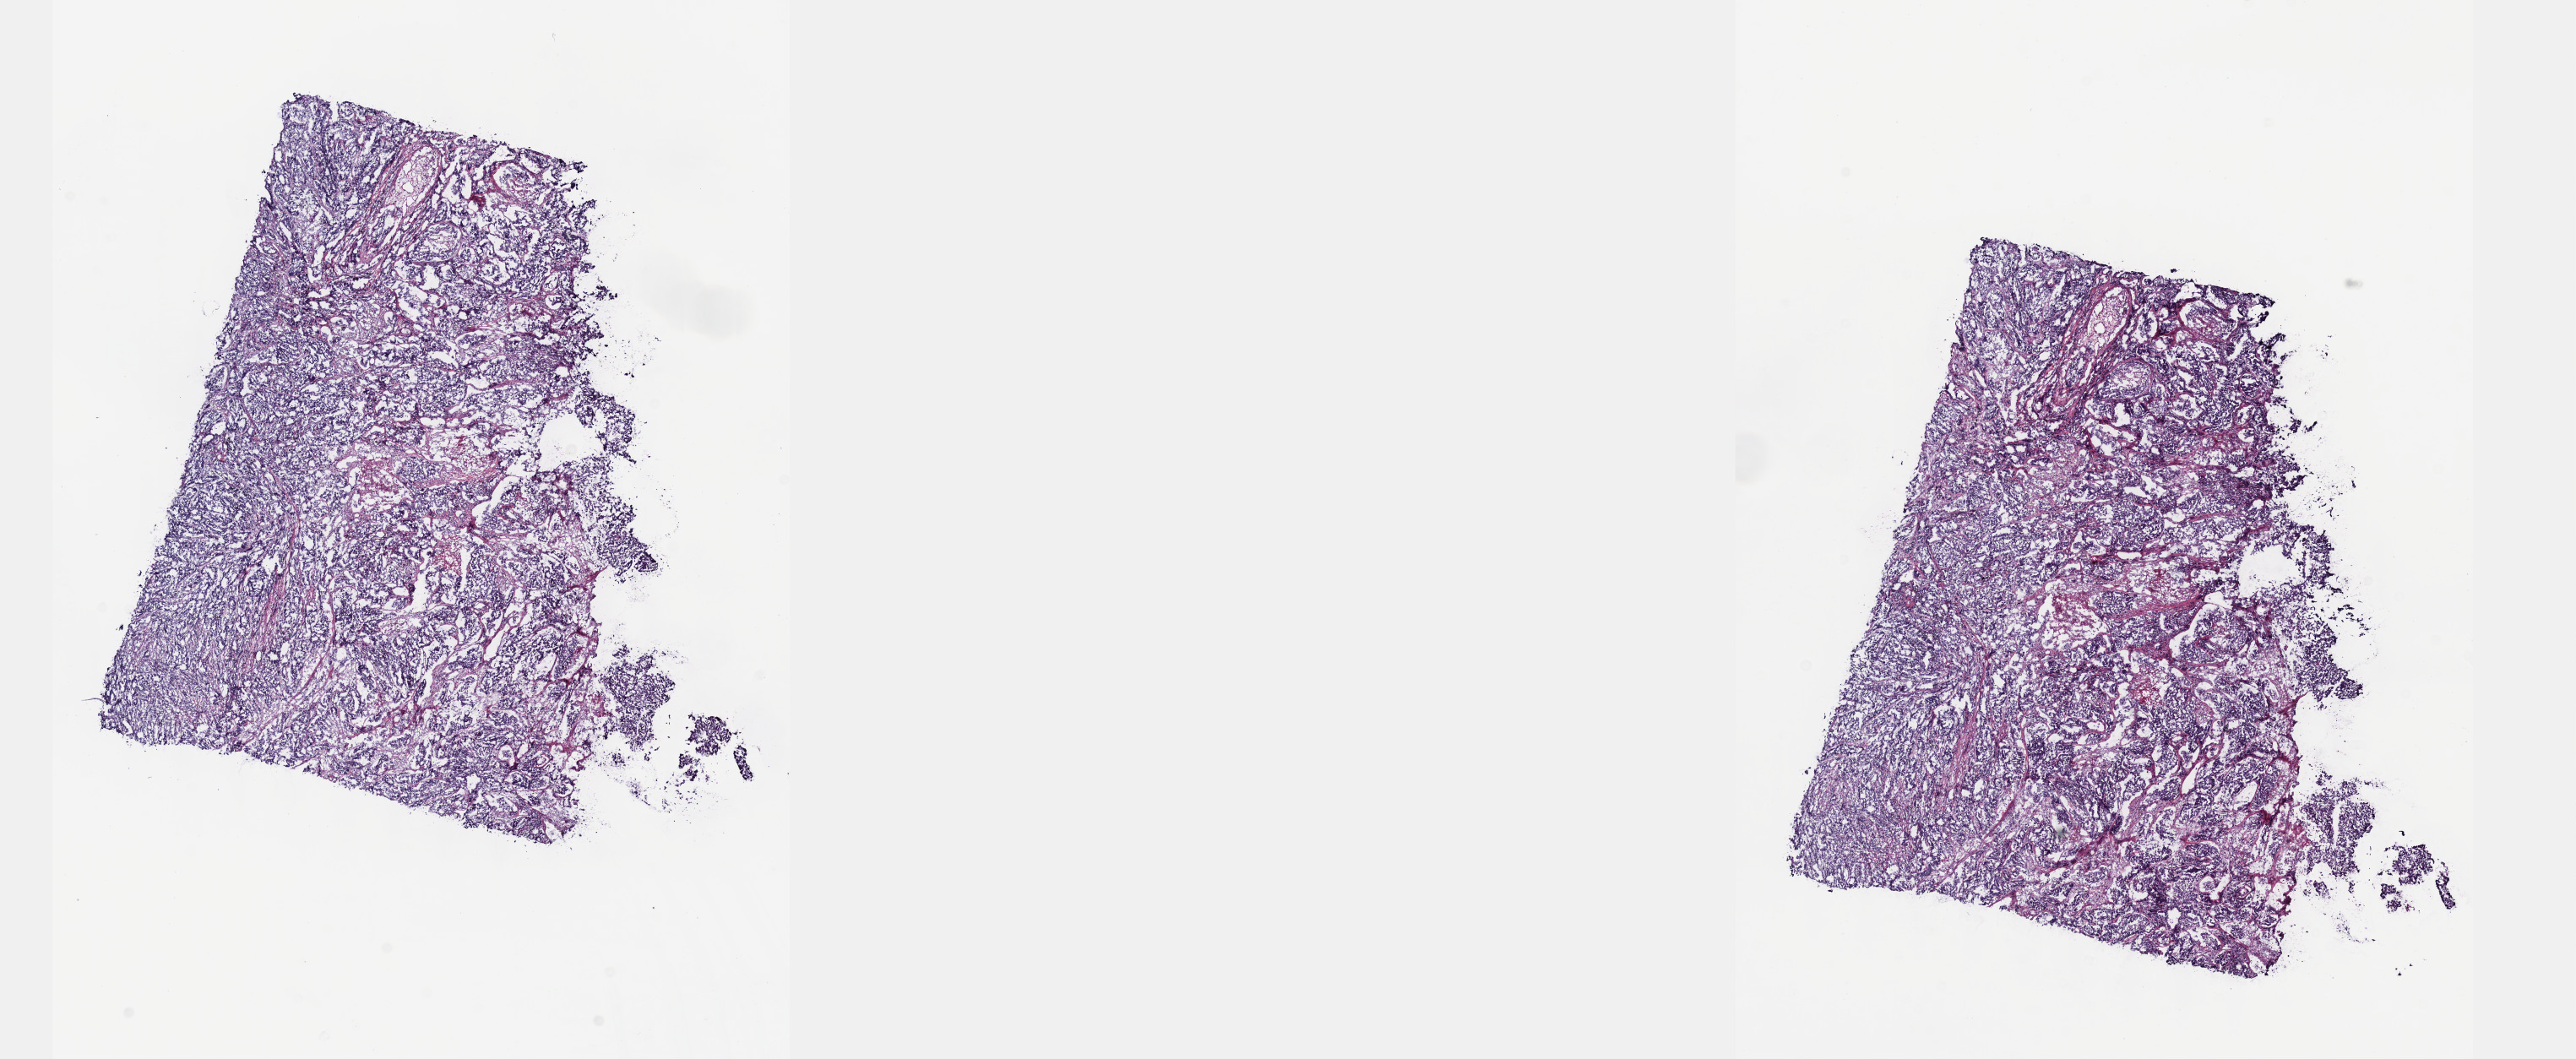
H&E-stained whole-slide image, low-resolution overview of the scanned area, about 24.6 x 10.1 mm (slide scanned at 40x). Frozen section from the top of the tissue portion. Sample: primary tumour, lung. Female patient; age at initial diagnosis 52 years. Pathologist review of this section (percent, as recorded): tumour cells 80%, tumour nuclei 90%, normal cells 0%, stromal cells 0%, necrosis 20%. Infiltration values recorded for this section: lymphocyte infiltration 0%, monocyte infiltration 0%, neutrophil infiltration 0%.
• laterality: right
• AJCC pathologic stage: IA (7th edition)
• pathologic diagnosis: Adenocarcinoma, NOS (lower lobe, lung)